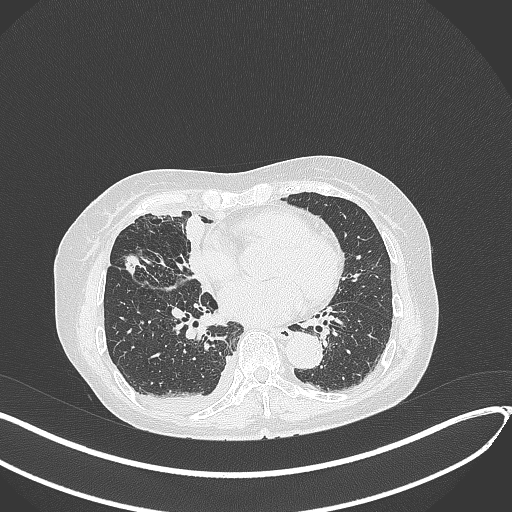
Chest CT, one axial slice. Slice 166 of 418 in the series (ordered by position). Reconstruction kernel B70f. 120 kVp. Lung window (W 1500 / L -600 HU). 1 mm slice thickness. 512 × 512 image matrix. Patient: female, 75 years. Case-level facts recorded for this patient, not image findings: clinical TNM (as recorded): T2a N3 M0.
Outlined on this slice (bounding box drawn by a radiologist):
- lung tumour (recorded histology: adenocarcinoma): bounding box <123,251,144,280> (left, top, right, bottom; pixels)